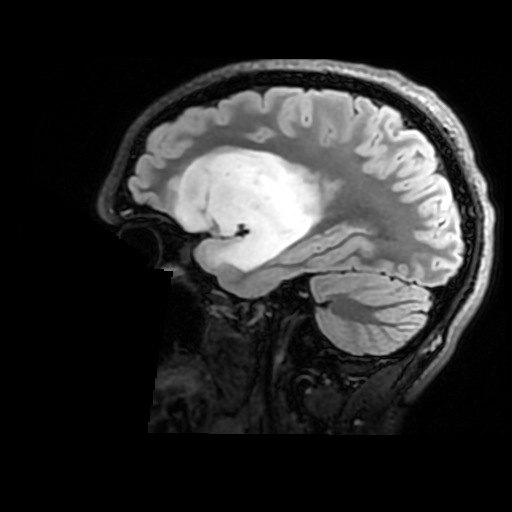
Brain MRI from a brain-tumour surgery series, one sagittal slice. Position 119 of 176 along the scan axis. T2 FLAIR. 1 mm slice thickness. 512 × 512 image matrix. From the clinical record (not read from this slice): histopathology: Astrocytoma; WHO grade: 2; IDH mutation: yes; tumour location: Right Insular.
Structures marked on this image (expert manual segmentation):
- tumour: bounding box <176,147,321,273> (left, top, right, bottom; pixels)